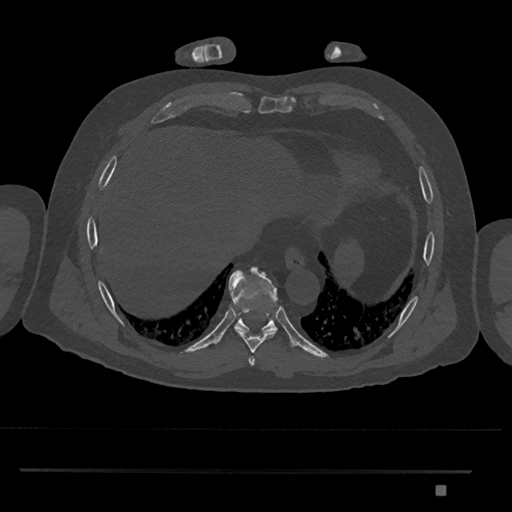
CT including the spine, one axial slice; slice 1085 of 1134 in the series (ordered by position); bone window (W 1800 / L 400 HU); 512 × 512 image matrix. Patient: male, 65 years. Case-level facts recorded for this patient, not image findings: primary cancer: prostate.
Annotated regions visible in this slice (semi-automatic segmentation, software-assisted and operator-edited):
- T8 vertebra: bounding box (x1, y1, x2, y2) in pixels: (235, 329, 276, 354)
- T9 vertebra: (229, 267, 278, 334)